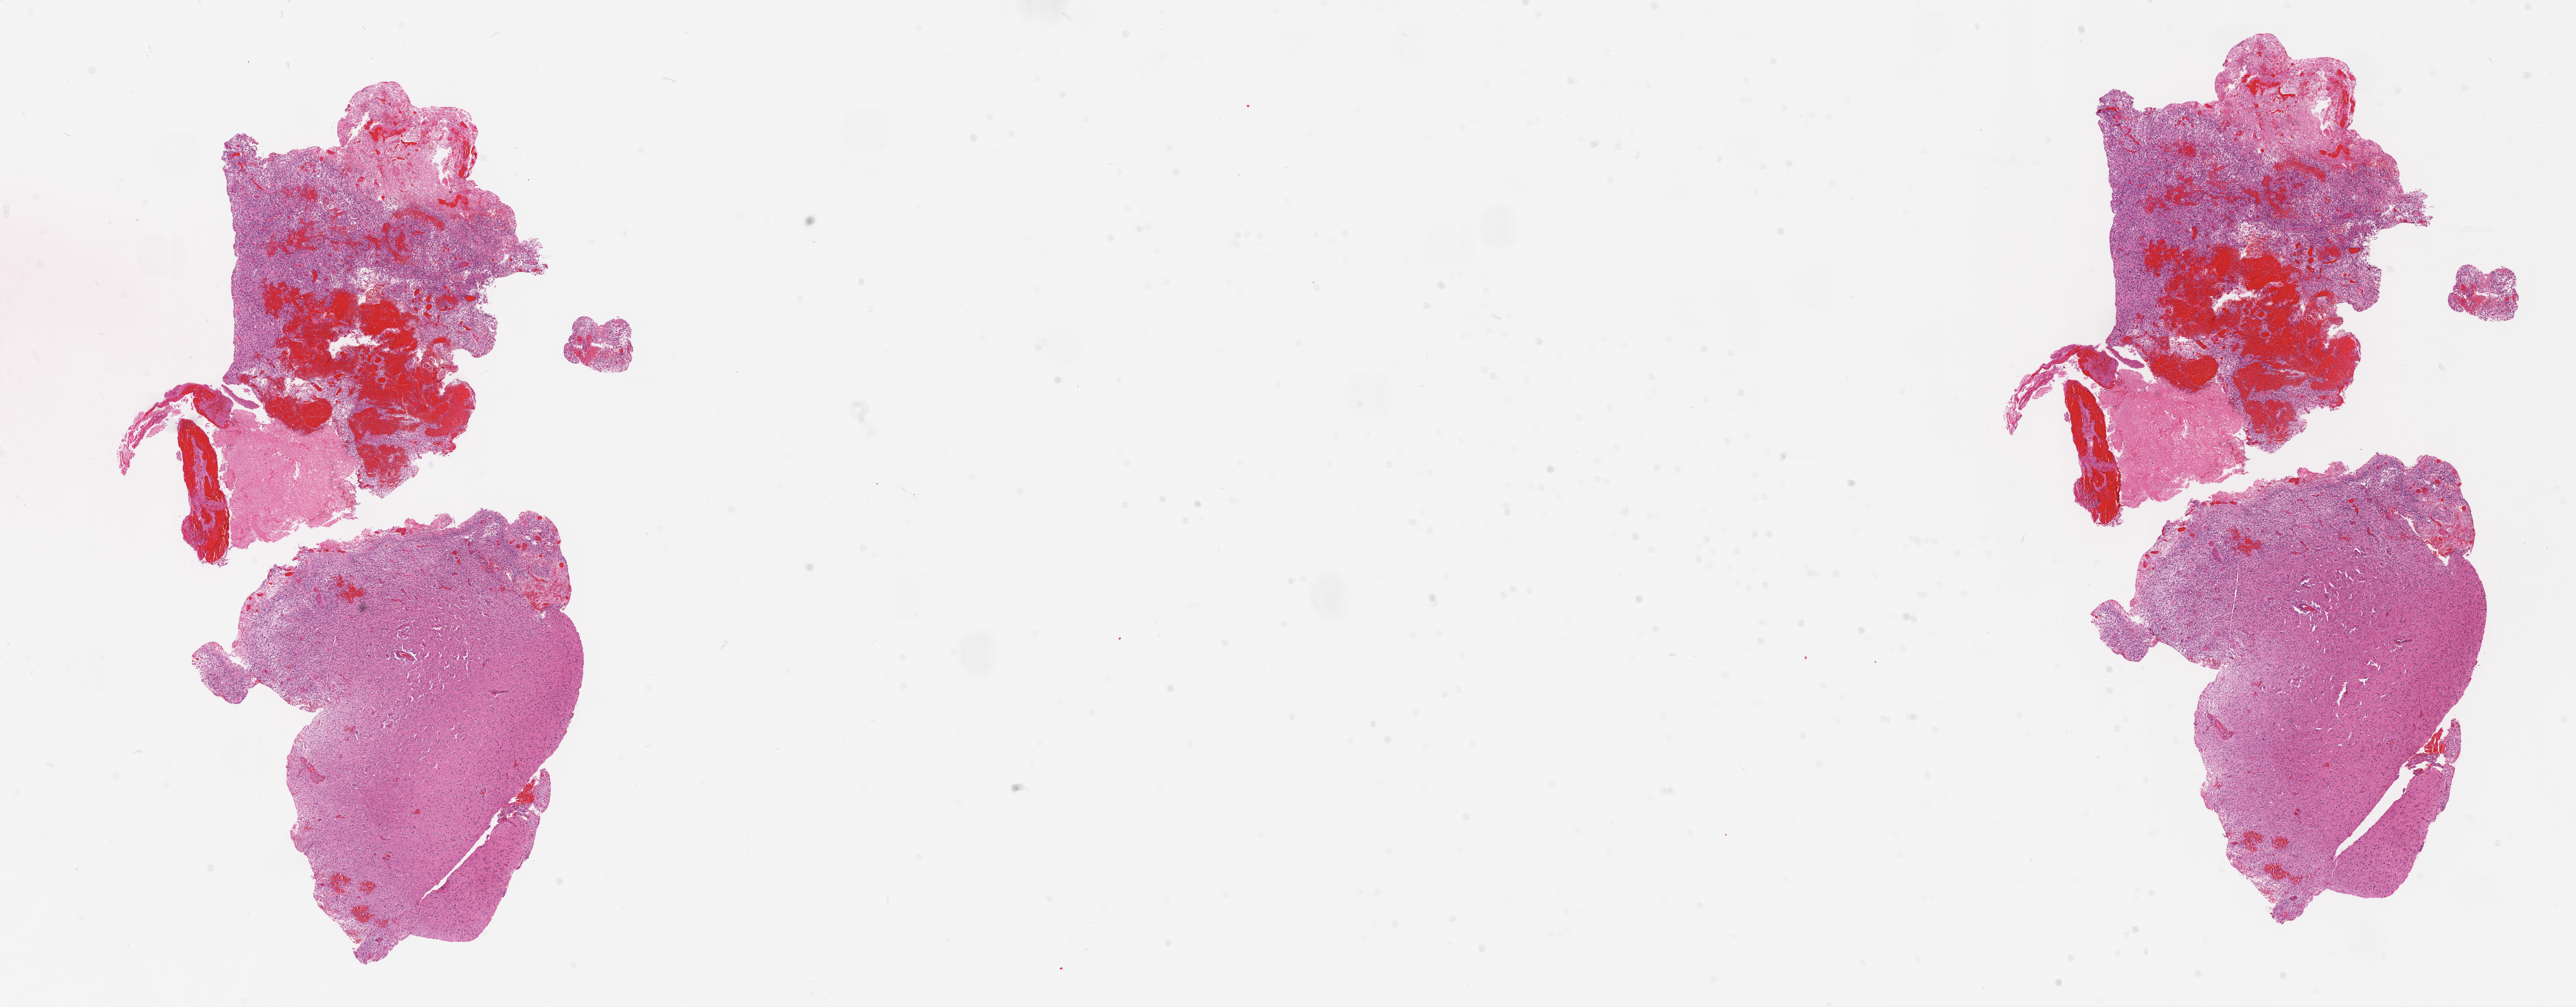
Digitized H&E-stained tissue section (whole slide) — shown as a low-resolution overview of the whole scanned area (about 30.1 x 11.8 mm, acquisition: 20x scan); formalin-fixed paraffin-embedded (FFPE) diagnostic section; primary tumour sample from the brain. Male, age 48 years at initial diagnosis.
Diagnosis: Glioblastoma.